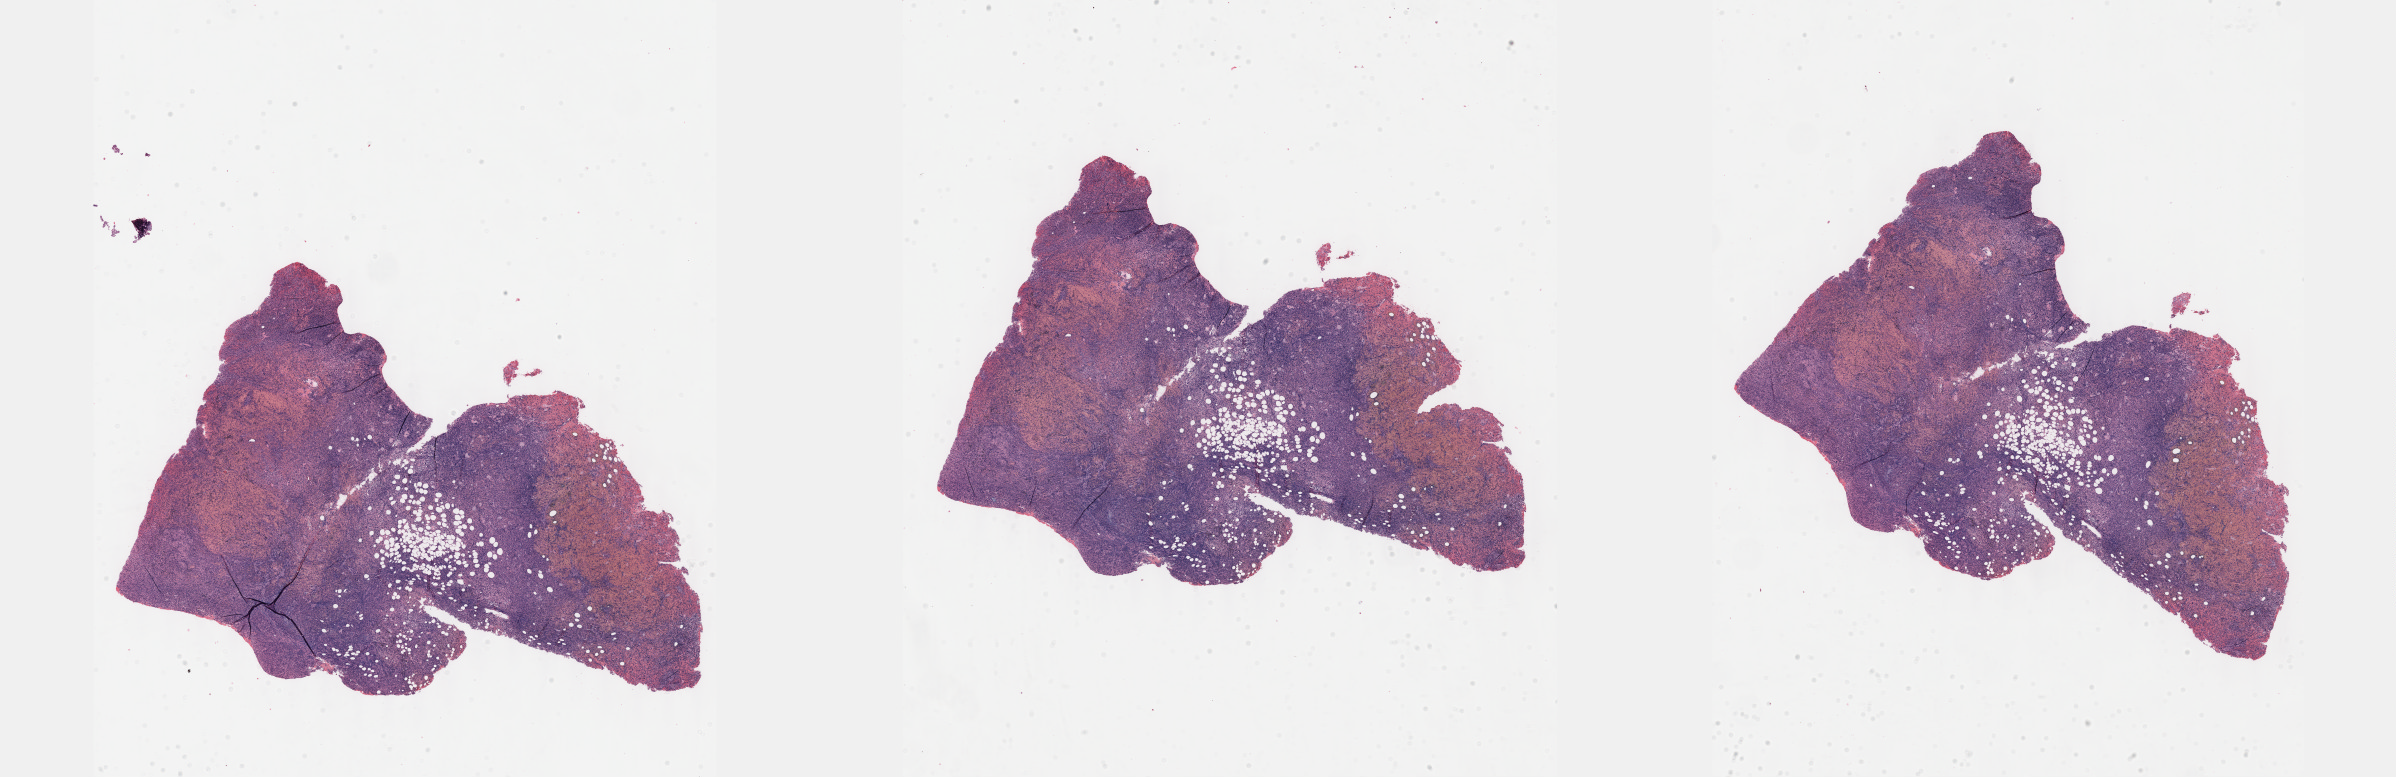
H&E whole-slide image — a low-resolution overview of the entire scanned area, about 38.7 x 12.6 mm (acquisition: 40x scan), formalin-fixed paraffin-embedded (FFPE) diagnostic section, sample: primary tumour, connective, subcutaneous and other soft tissues. Female, age 53 years at initial diagnosis.
Histologic diagnosis: Leiomyosarcoma, NOS (connective, subcutaneous and other soft tissues of thorax).